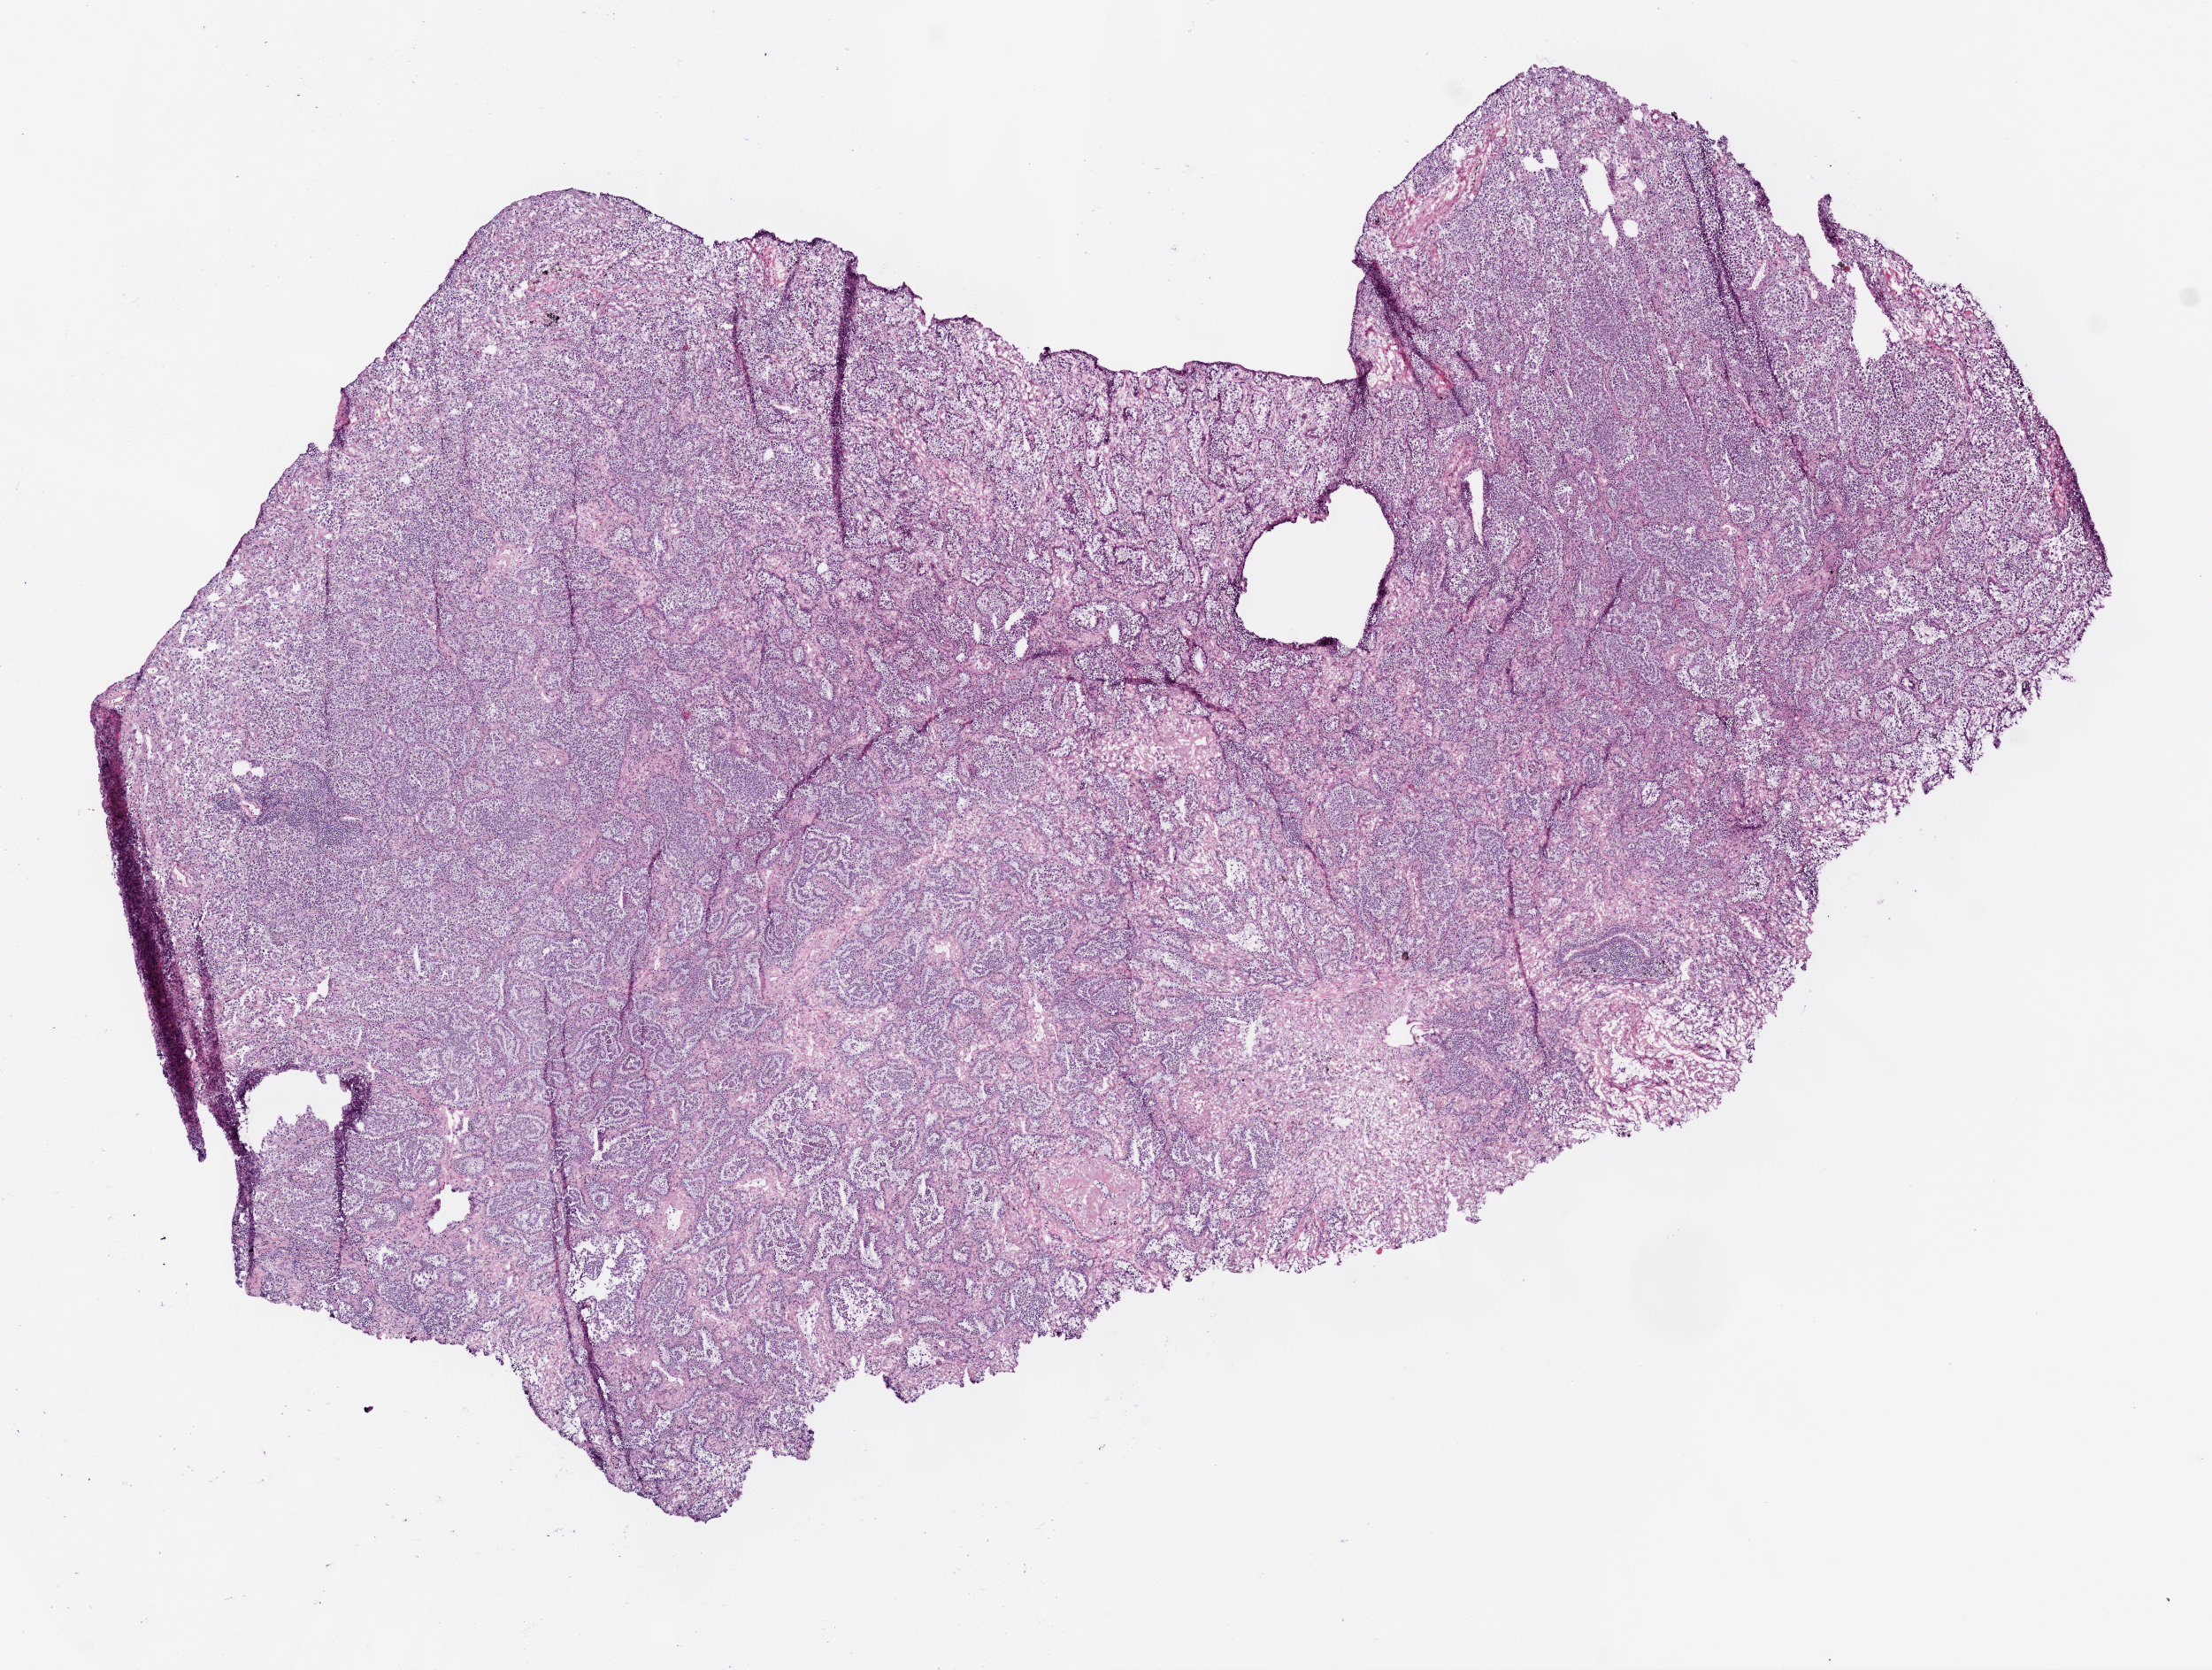
Whole-slide histology image, H&E, a low-resolution overview of the entire scanned area, about 10.0 x 7.6 mm; frozen section from the top of the tissue portion; sample: primary tumour, lung. Female patient; age at initial diagnosis 84 years. Pathologist review of this section (percent, as recorded): tumour cells 90%, tumour nuclei 80%, normal cells 0%, stromal cells 10%, necrosis 0%.
* TNM: T2 N0 M0
* laterality: left
* pathologic diagnosis: Adenocarcinoma, NOS (lower lobe, lung)
* AJCC pathologic stage: IB (6th edition)